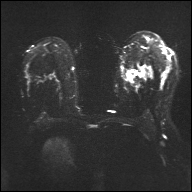
Breast MRI, one axial slice; slice 23 of 32 in the series (ordered by position); diffusion-weighted series; image 2 of 4 stored at this slice position (different b-values; order by instance number); 1.5 T; 4 mm slice thickness; 192 × 192 image matrix, field of view 360 × 360 mm. Female patient.
Annotated regions visible in this slice (expert manual segmentation):
- tumour on diffusion-weighted imaging: box from (x=139, y=72) to (x=145, y=77) px